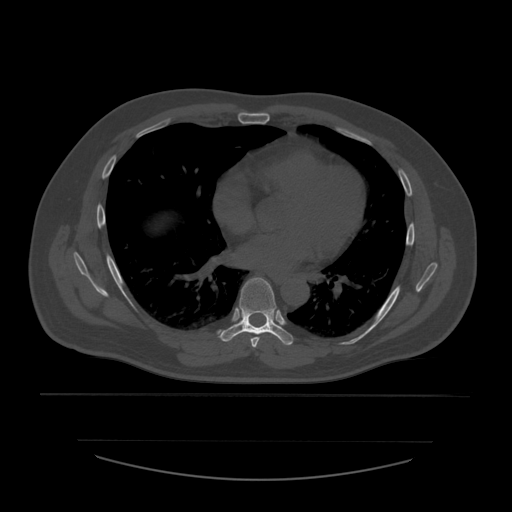
CT including the spine, one axial slice; slice 363 of 532 in the series (ordered by position); reconstruction kernel STANDARD; 120 kVp; bone window (W 1800 / L 400 HU); 1.25 mm slice thickness; 512 × 512 image matrix. Patient age 44 years. From the clinical record (not read from this slice): primary cancer: soft tissue sarcoma.
Annotated regions visible in this slice (semi-automatic segmentation, software-assisted and operator-edited):
- T6 vertebra: box from (x=250, y=333) to (x=260, y=348) px
- T7 vertebra: (x=219, y=278)–(x=294, y=346)